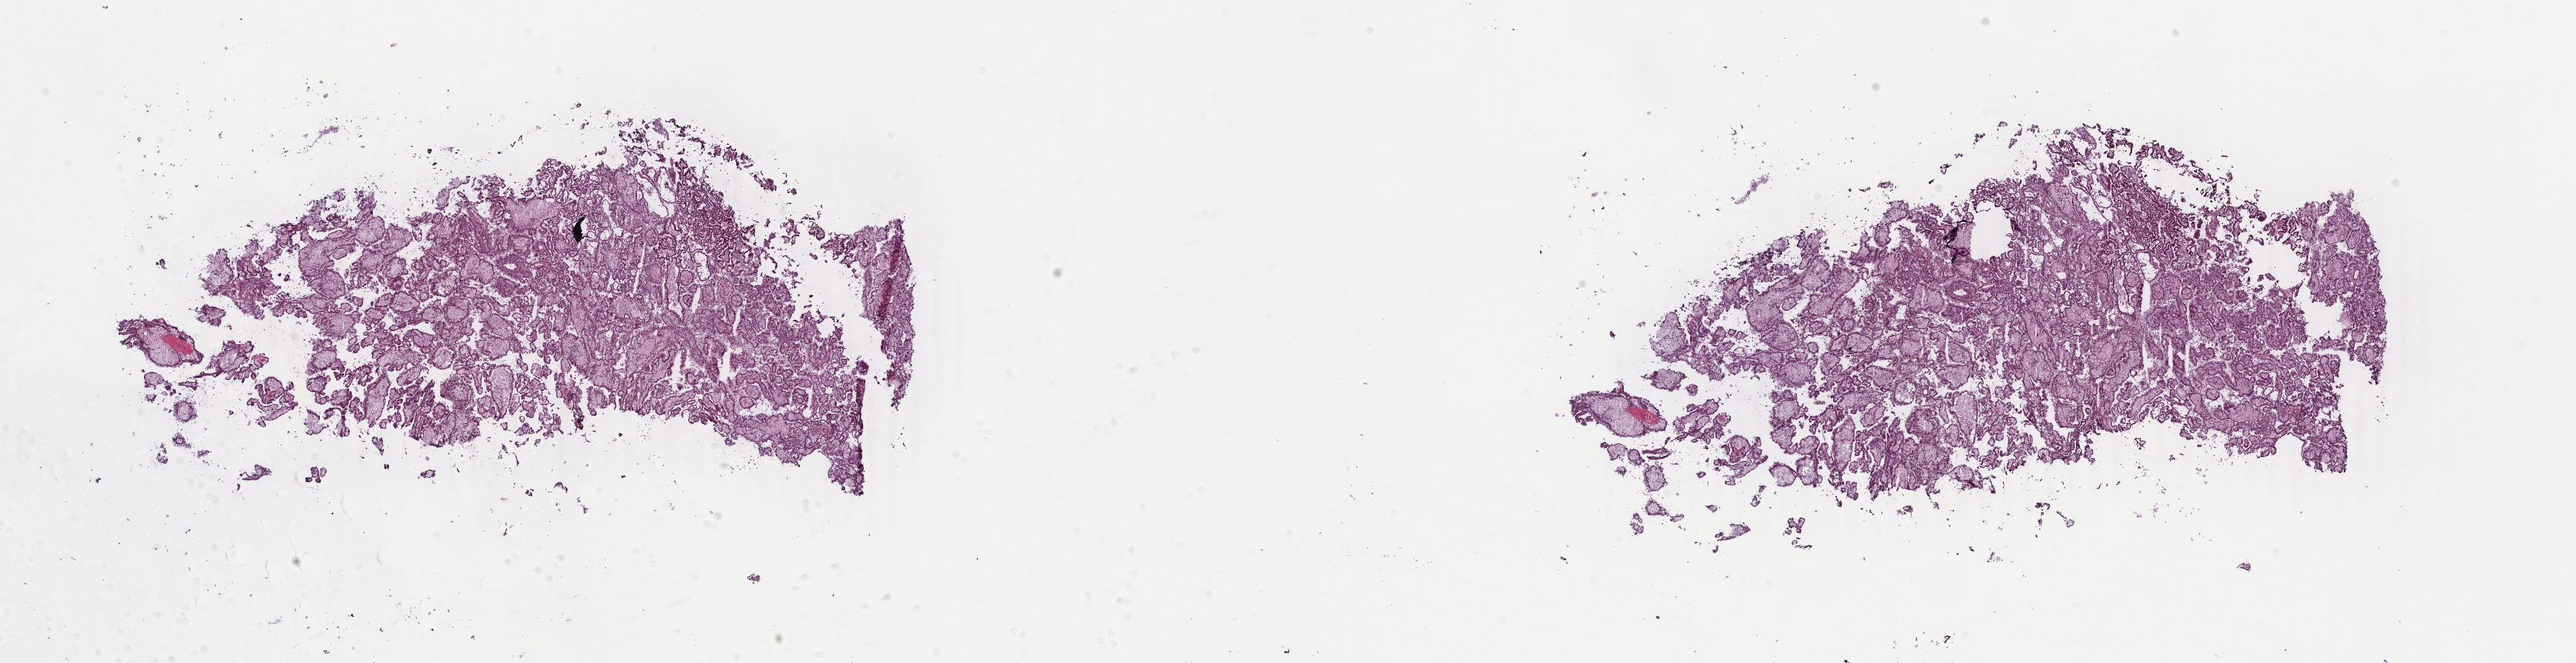
Digitized Hematoxylin and eosin (H&E) stained tissue section (whole slide) — a low-resolution overview of the entire scanned area, about 27.6 x 7.1 mm, frozen section from the top of the tissue portion, kidney, primary tumour sample. Male patient; age at initial diagnosis 51 years. Composition of this section per pathologist review: tumour cells 100%, tumour nuclei 75%, normal cells 0%, stromal cells 0%, necrosis 0%. Infiltration values recorded for this section: lymphocyte infiltration 2%, monocyte infiltration 5%, neutrophil infiltration 0%.
AJCC pathologic stage: I (7th edition). Laterality: right. Pathologic diagnosis: Papillary adenocarcinoma, NOS.